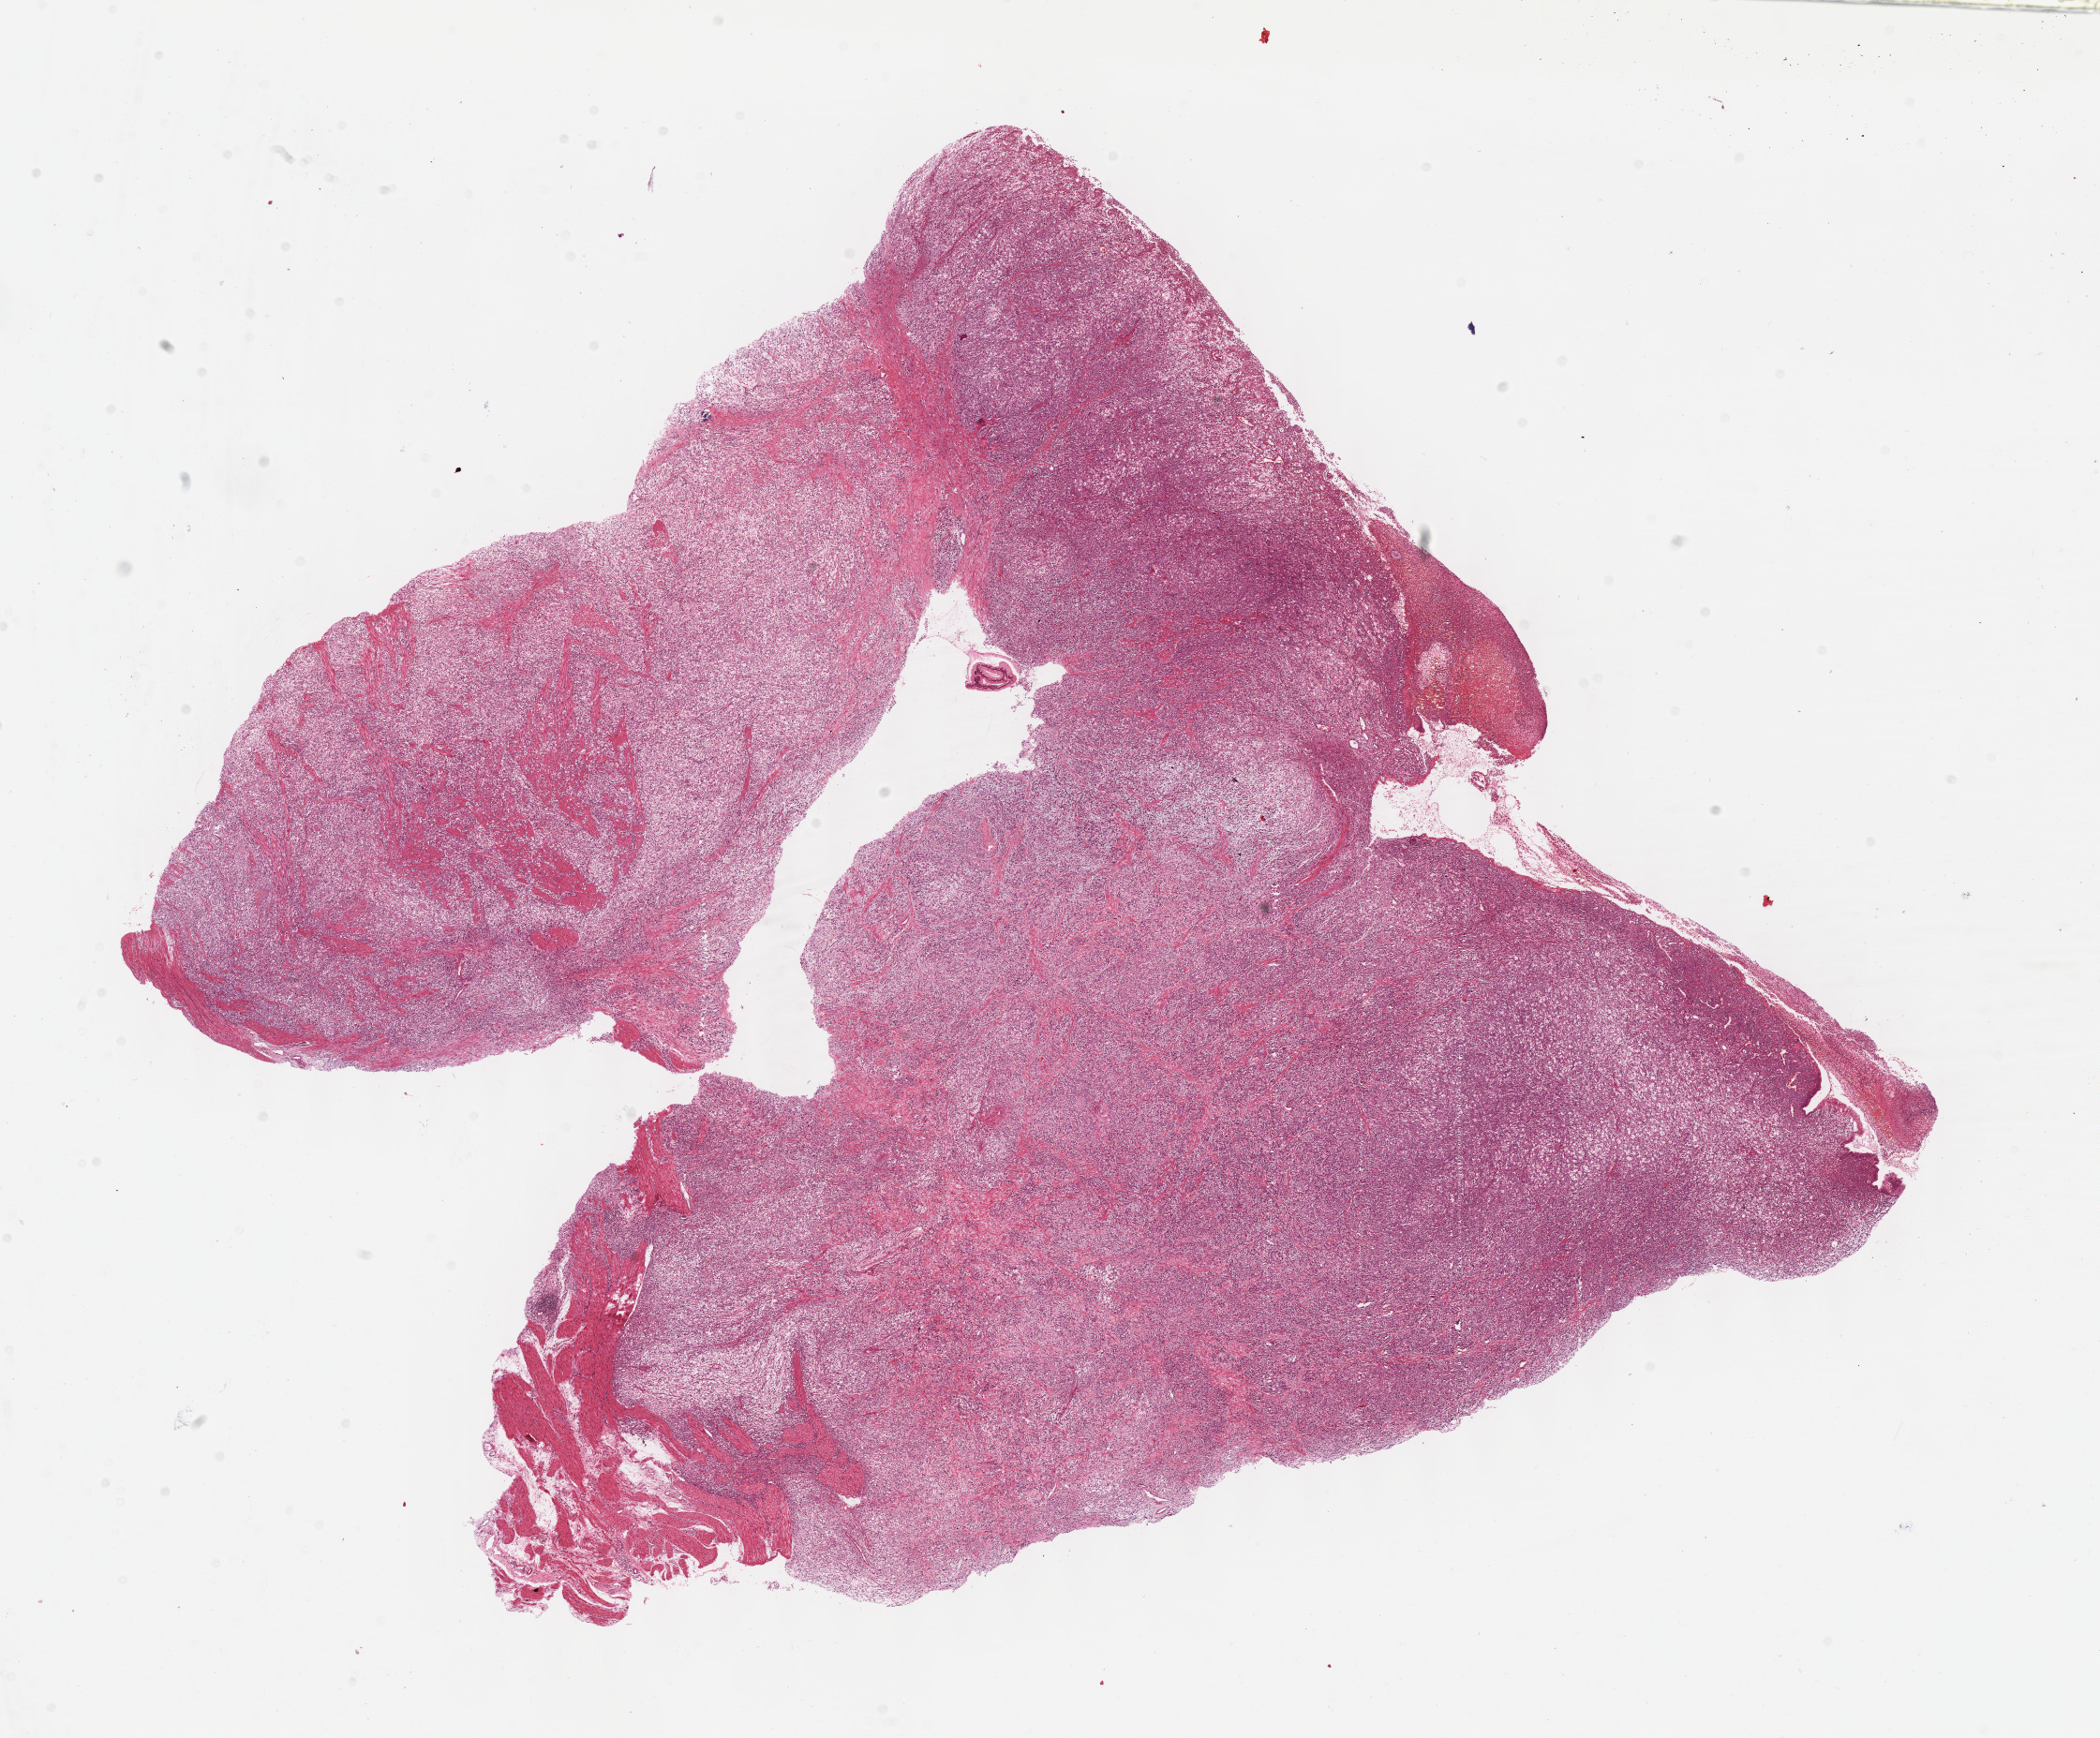
Whole-slide histology image, H&E-stained, low-resolution overview of the scanned area, about 18.1 x 15.0 mm (acquisition: 40x scan); formalin-fixed paraffin-embedded (FFPE) diagnostic section; sample: primary tumour, stomach. Patient: male, age at initial diagnosis 41 years. Histologic grade: G3 (poorly differentiated).
- AJCC pathologic stage: II (6th edition)
- histologic diagnosis: Carcinoma, diffuse type (gastric antrum)
- TNM: T3 N0 M0